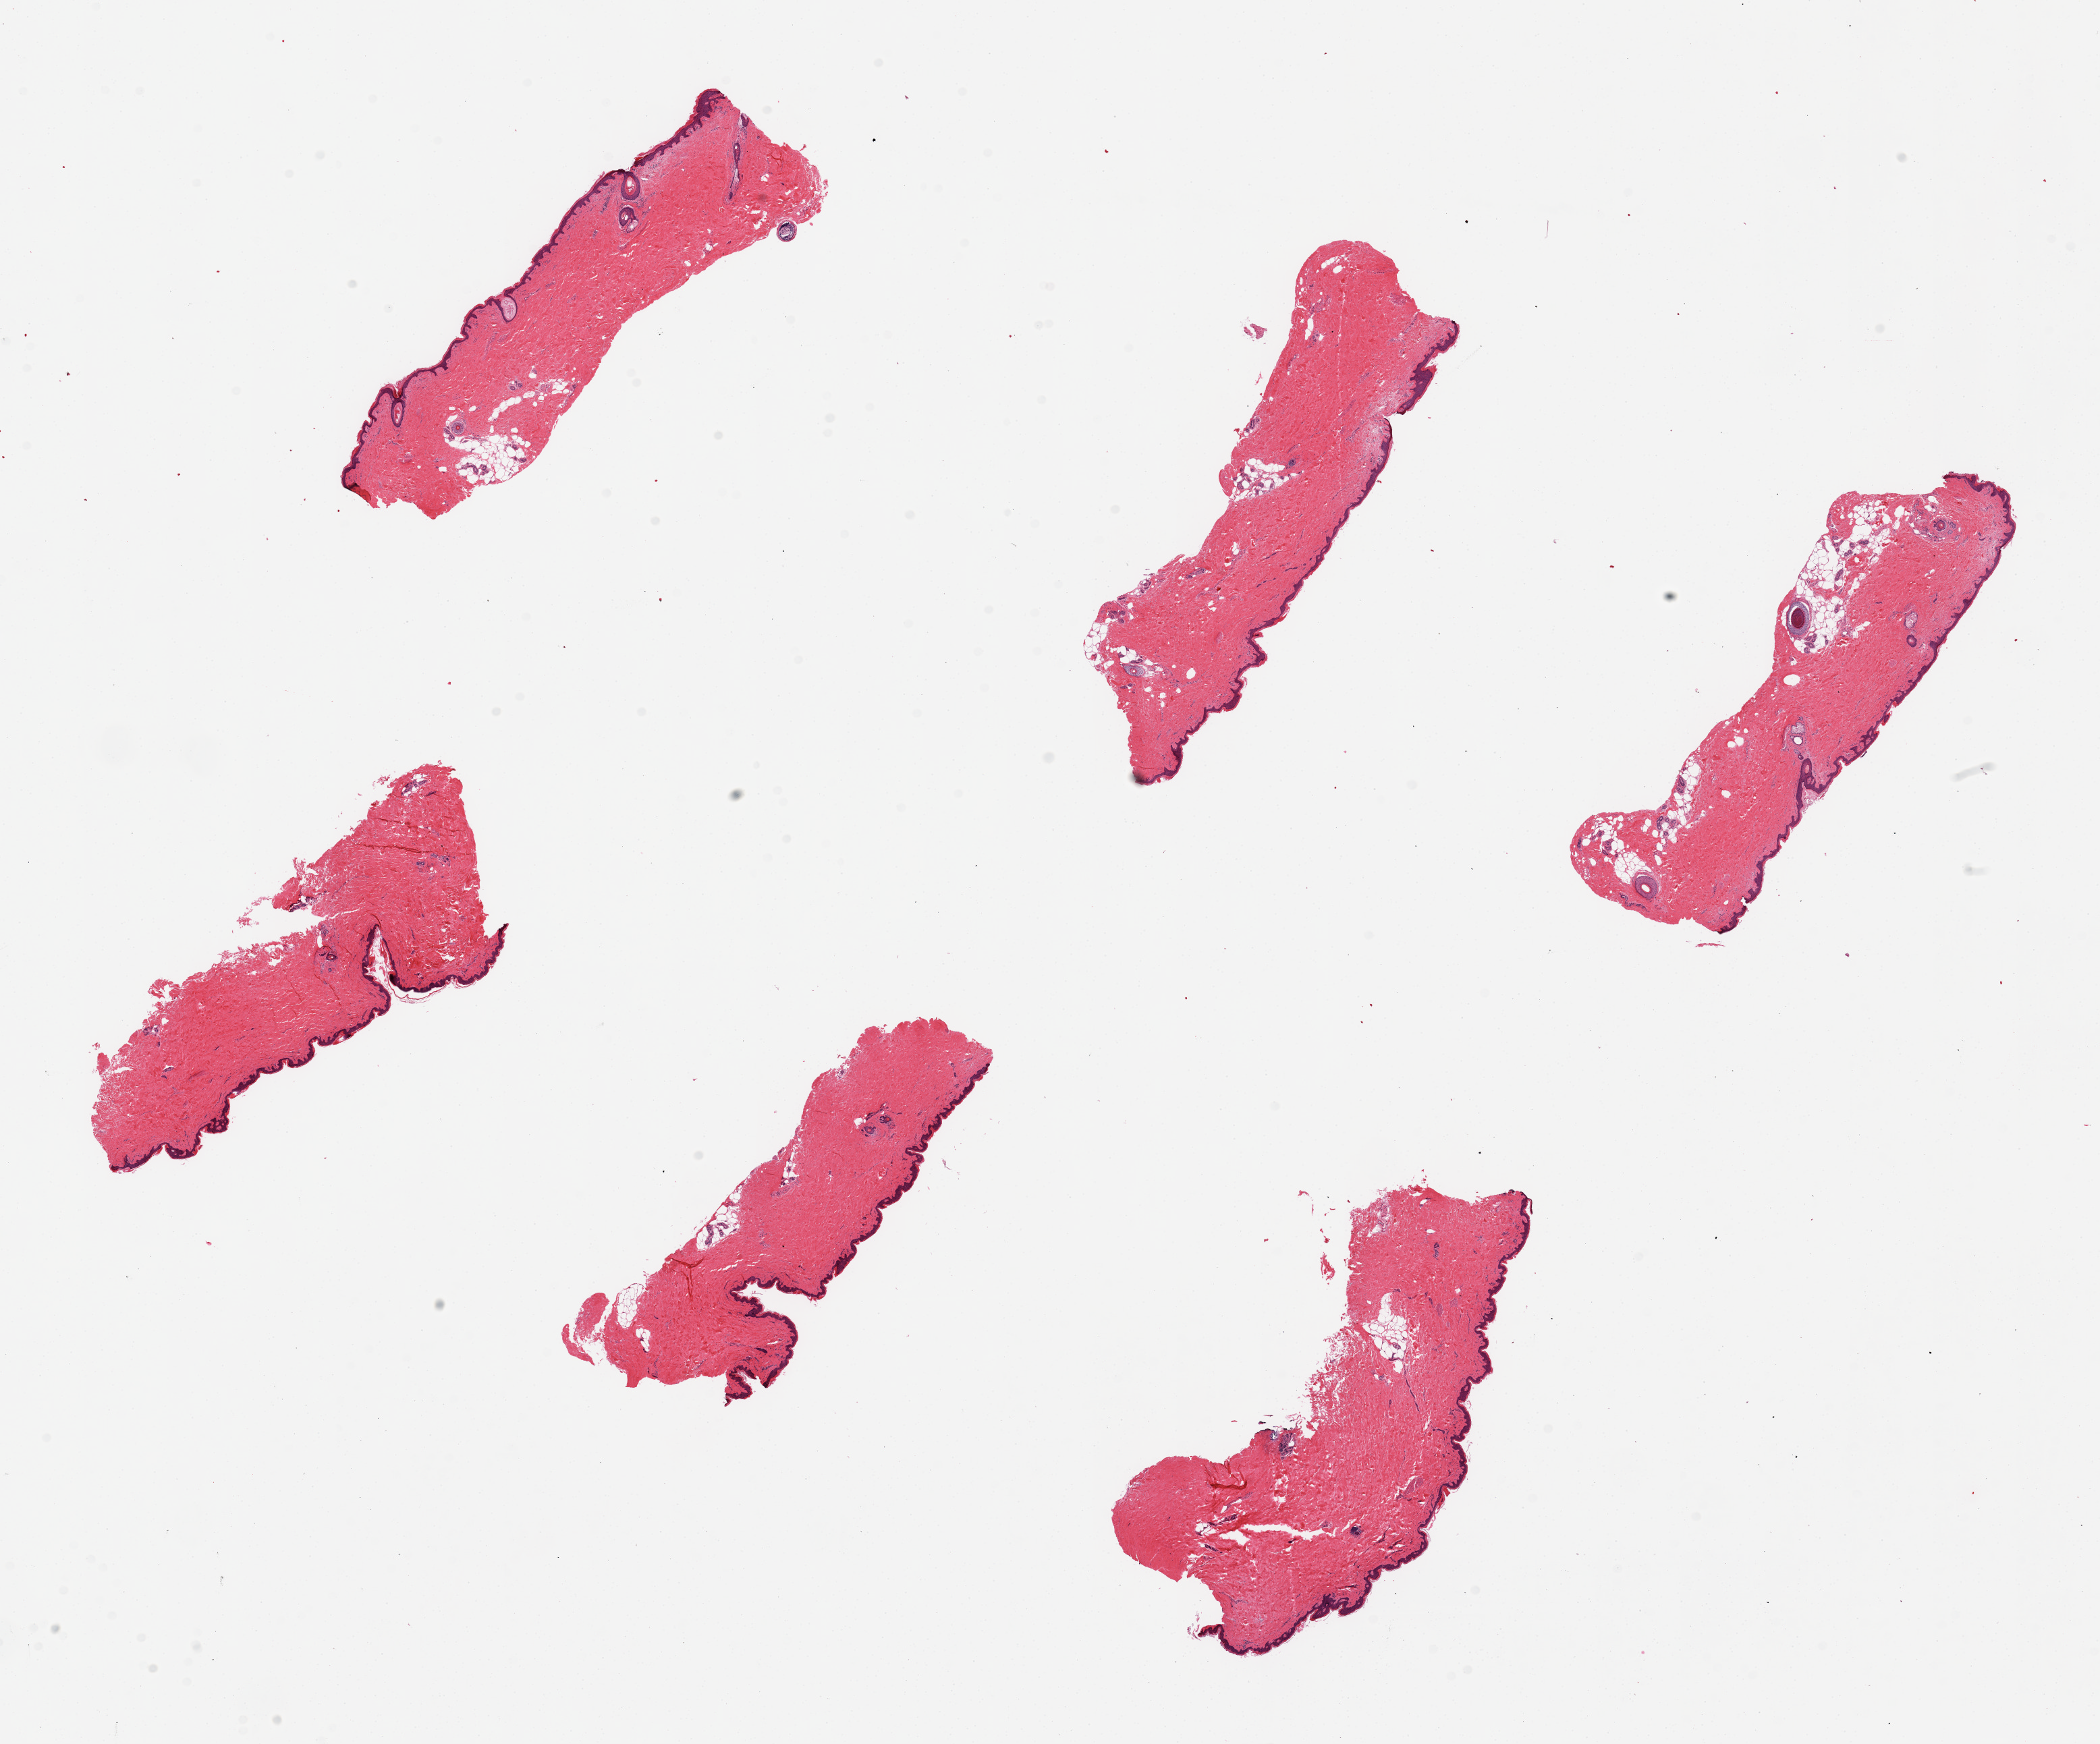
H&E whole-slide image, brightfield — whole scanned area (about 24.6 x 20.4 mm, slide scanned at 20x) shown as a low-resolution overview. PAXgene-fixed paraffin-embedded (PFPE) section. Section of skin of suprapubic region (target tissue). Donor tissue sample. Donor sex: female.
Pathologist's review note for this sample: 6 pieces, well trimmed with limited internal fat (up to 10%).